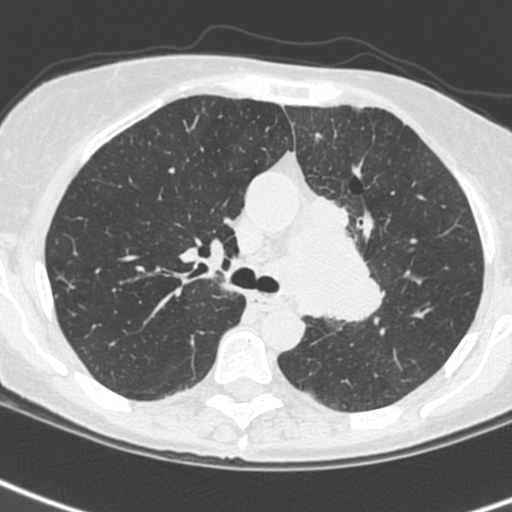
Low-dose screening chest CT, one axial slice. Slice 162 of 242 in the series (ordered by position). Lung window (W 1500 / L -600 HU). 1.3 mm slice thickness. 512 × 512 image matrix, field of view 284 × 284 mm.
Structures marked on this image (manually delineated by an expert):
- lesion 3 (tumor, upper lobe of left lung): bounding box (x1, y1, x2, y2) in pixels: (305, 193, 384, 322)